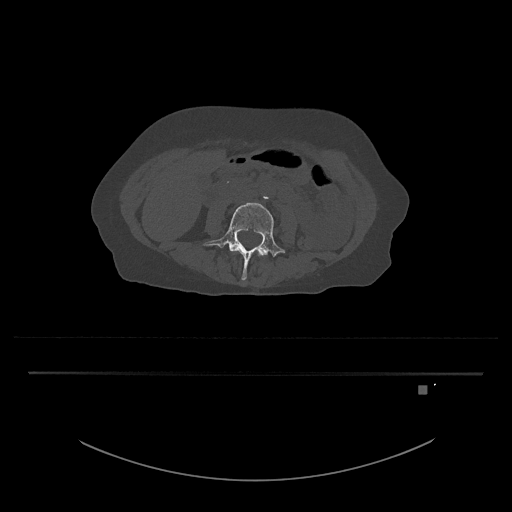
CT including the spine, one axial slice. Position 370 of 797 along the scan axis. Reconstruction kernel Br40s/3. Bone window (W 1800 / L 400 HU). 512 × 512 image matrix, field of view 500 × 500 mm. Female patient, age 57 years. Case-level facts recorded for this patient, not image findings: primary cancer: cervical.
Annotated regions visible in this slice (semi-automatic segmentation, software-assisted and operator-edited):
- L3 vertebra: bounding box (x1, y1, x2, y2) in pixels: (258, 251, 263, 257)
- L4 vertebra: (203, 202, 286, 280)